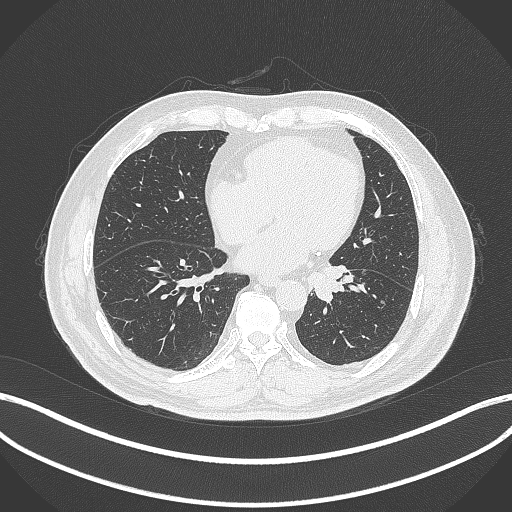
Chest CT, one axial slice; slice 100 of 312 in the series (ordered by position); reconstruction kernel B70f; lung window (W 1500 / L -600 HU); 512 × 512 image matrix, field of view 400 × 400 mm. Patient: male, 71 years. Case-level facts recorded for this patient, not image findings: clinical TNM (as recorded): T1b N0 M0.
Structures marked on this image (bounding box drawn by a radiologist):
- lung tumour (recorded histology: squamous cell carcinoma): bounding box [x1, y1, x2, y2] px = [306, 258, 347, 303]